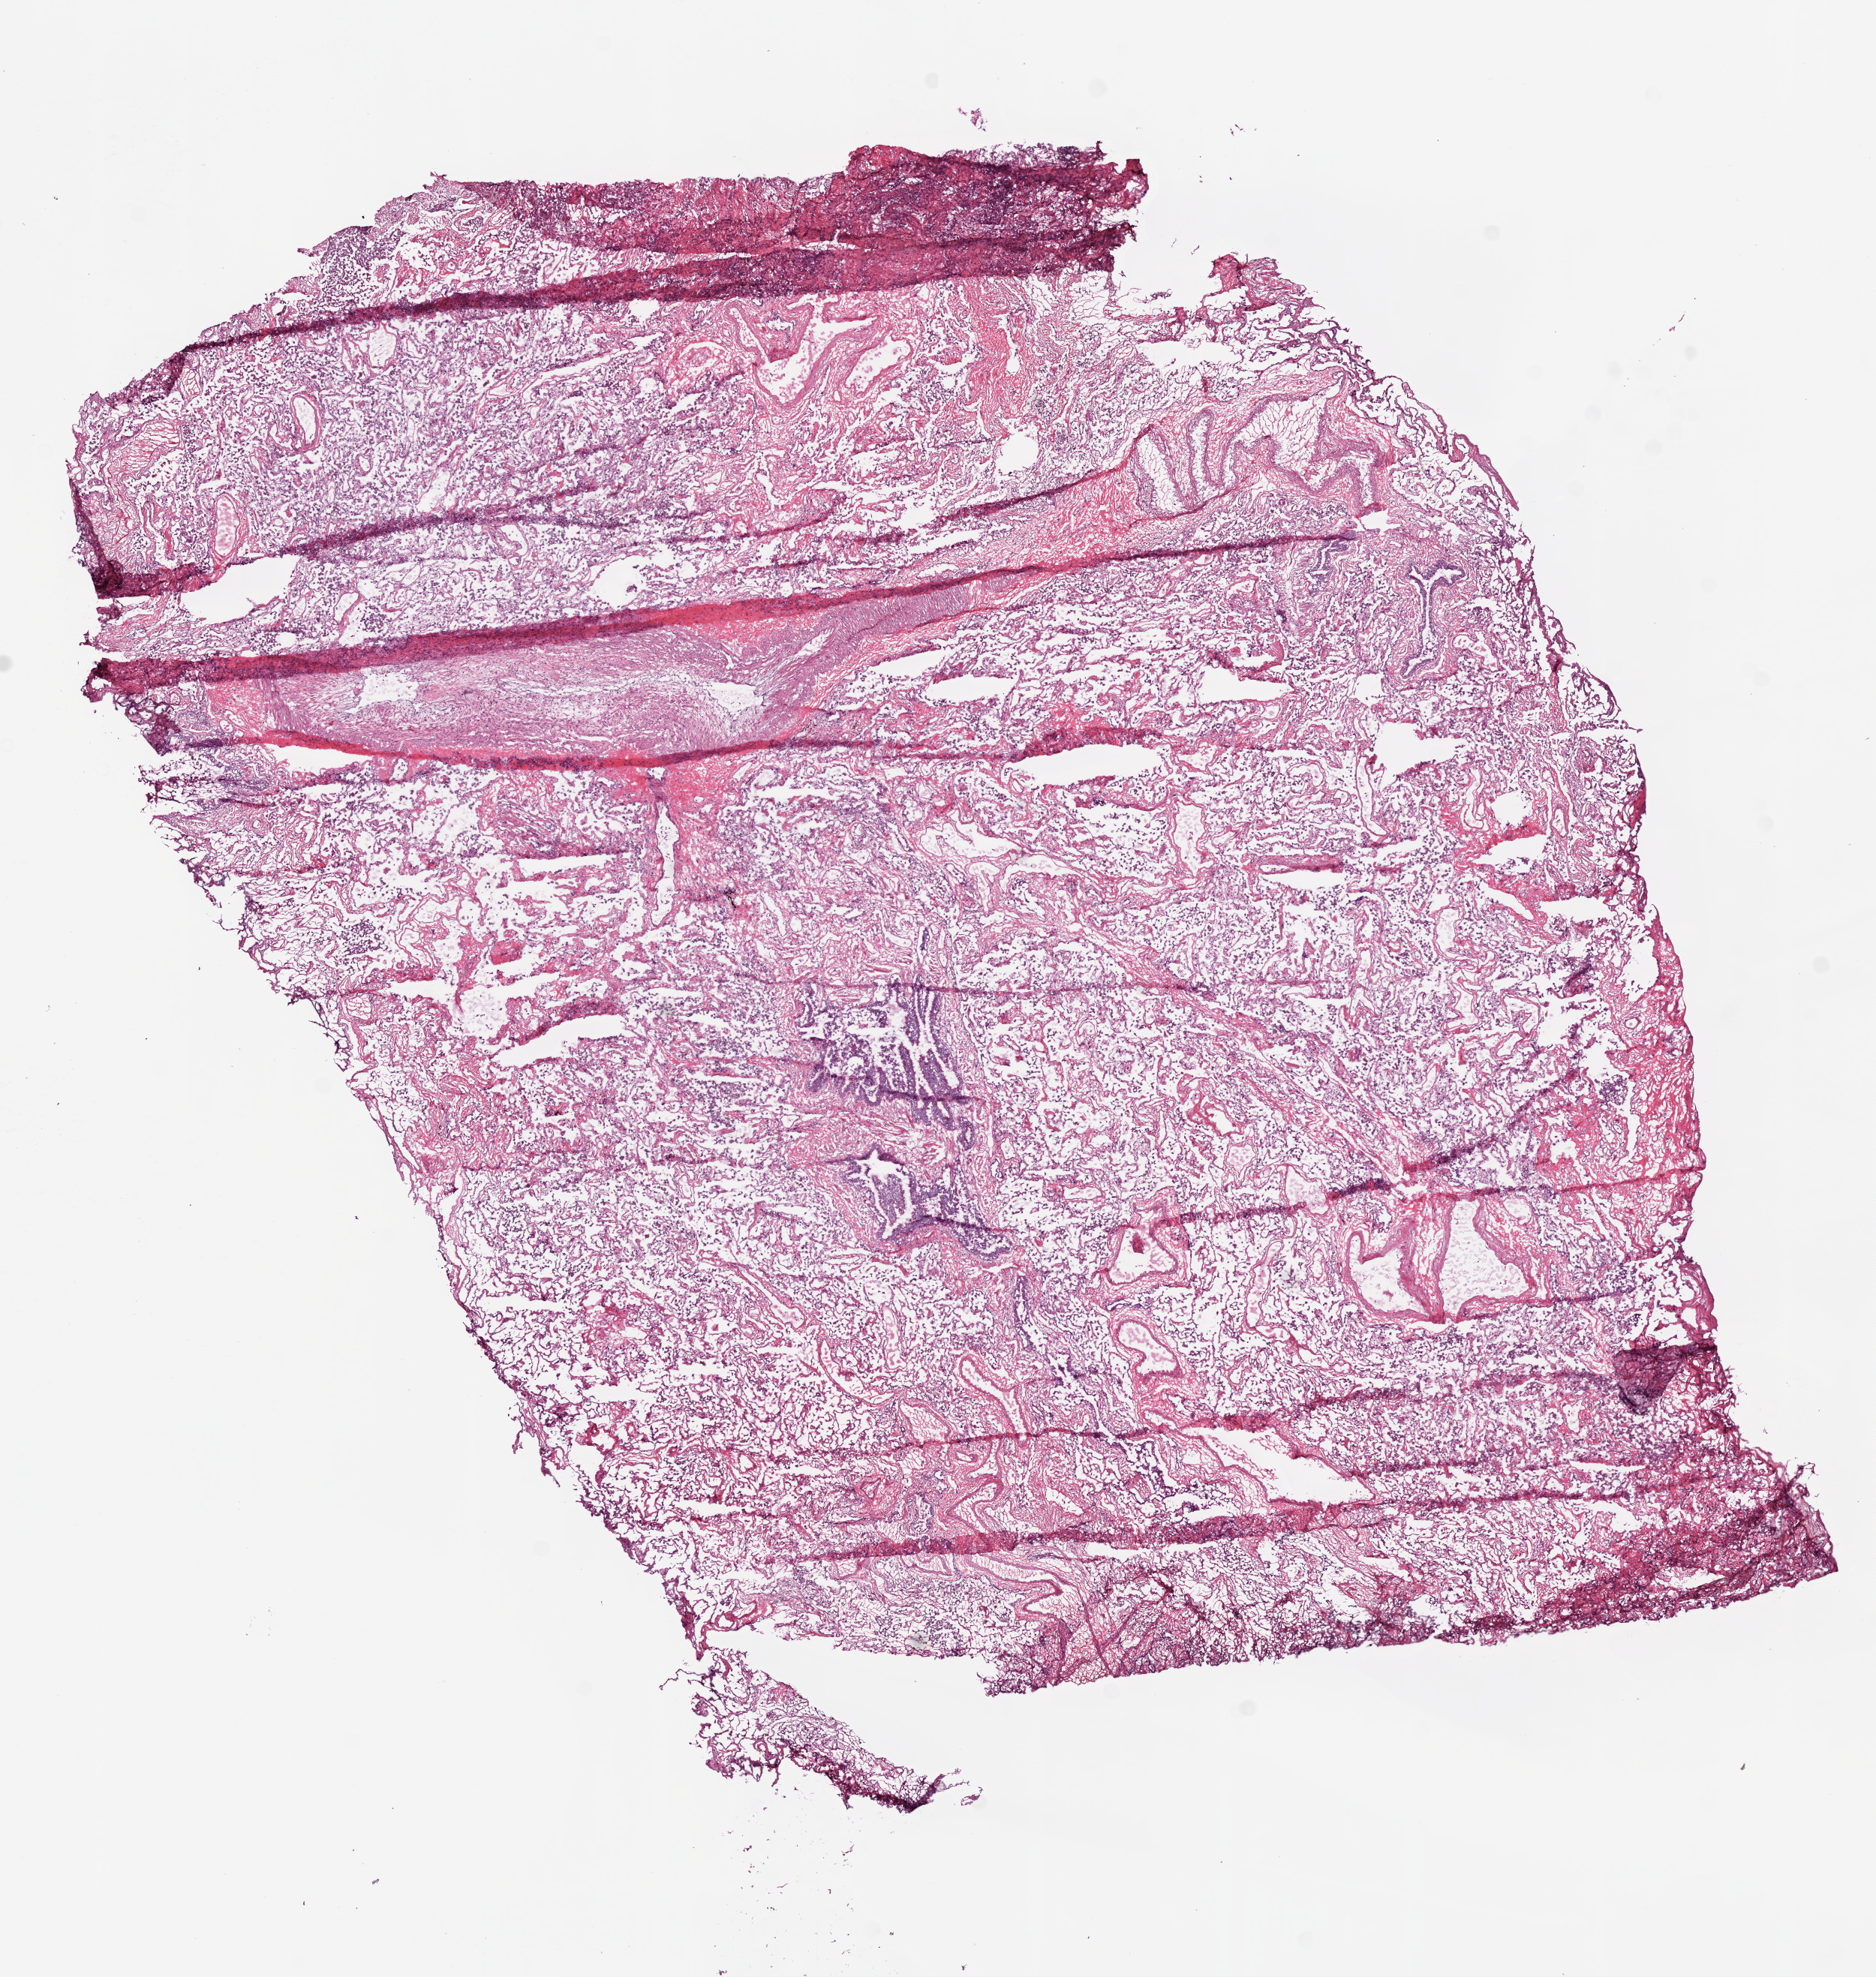
Whole-slide histology image, Hematoxylin and eosin (H&E) stained, low-resolution overview of the scanned area, about 10.0 x 10.6 mm. Frozen section. Lung, solid tissue normal (non-tumour tissue) sample. Female patient; age at initial diagnosis 64 years.
- this section: solid tissue normal sample (biorepository sample class)
- patient diagnosis: Squamous cell carcinoma, NOS